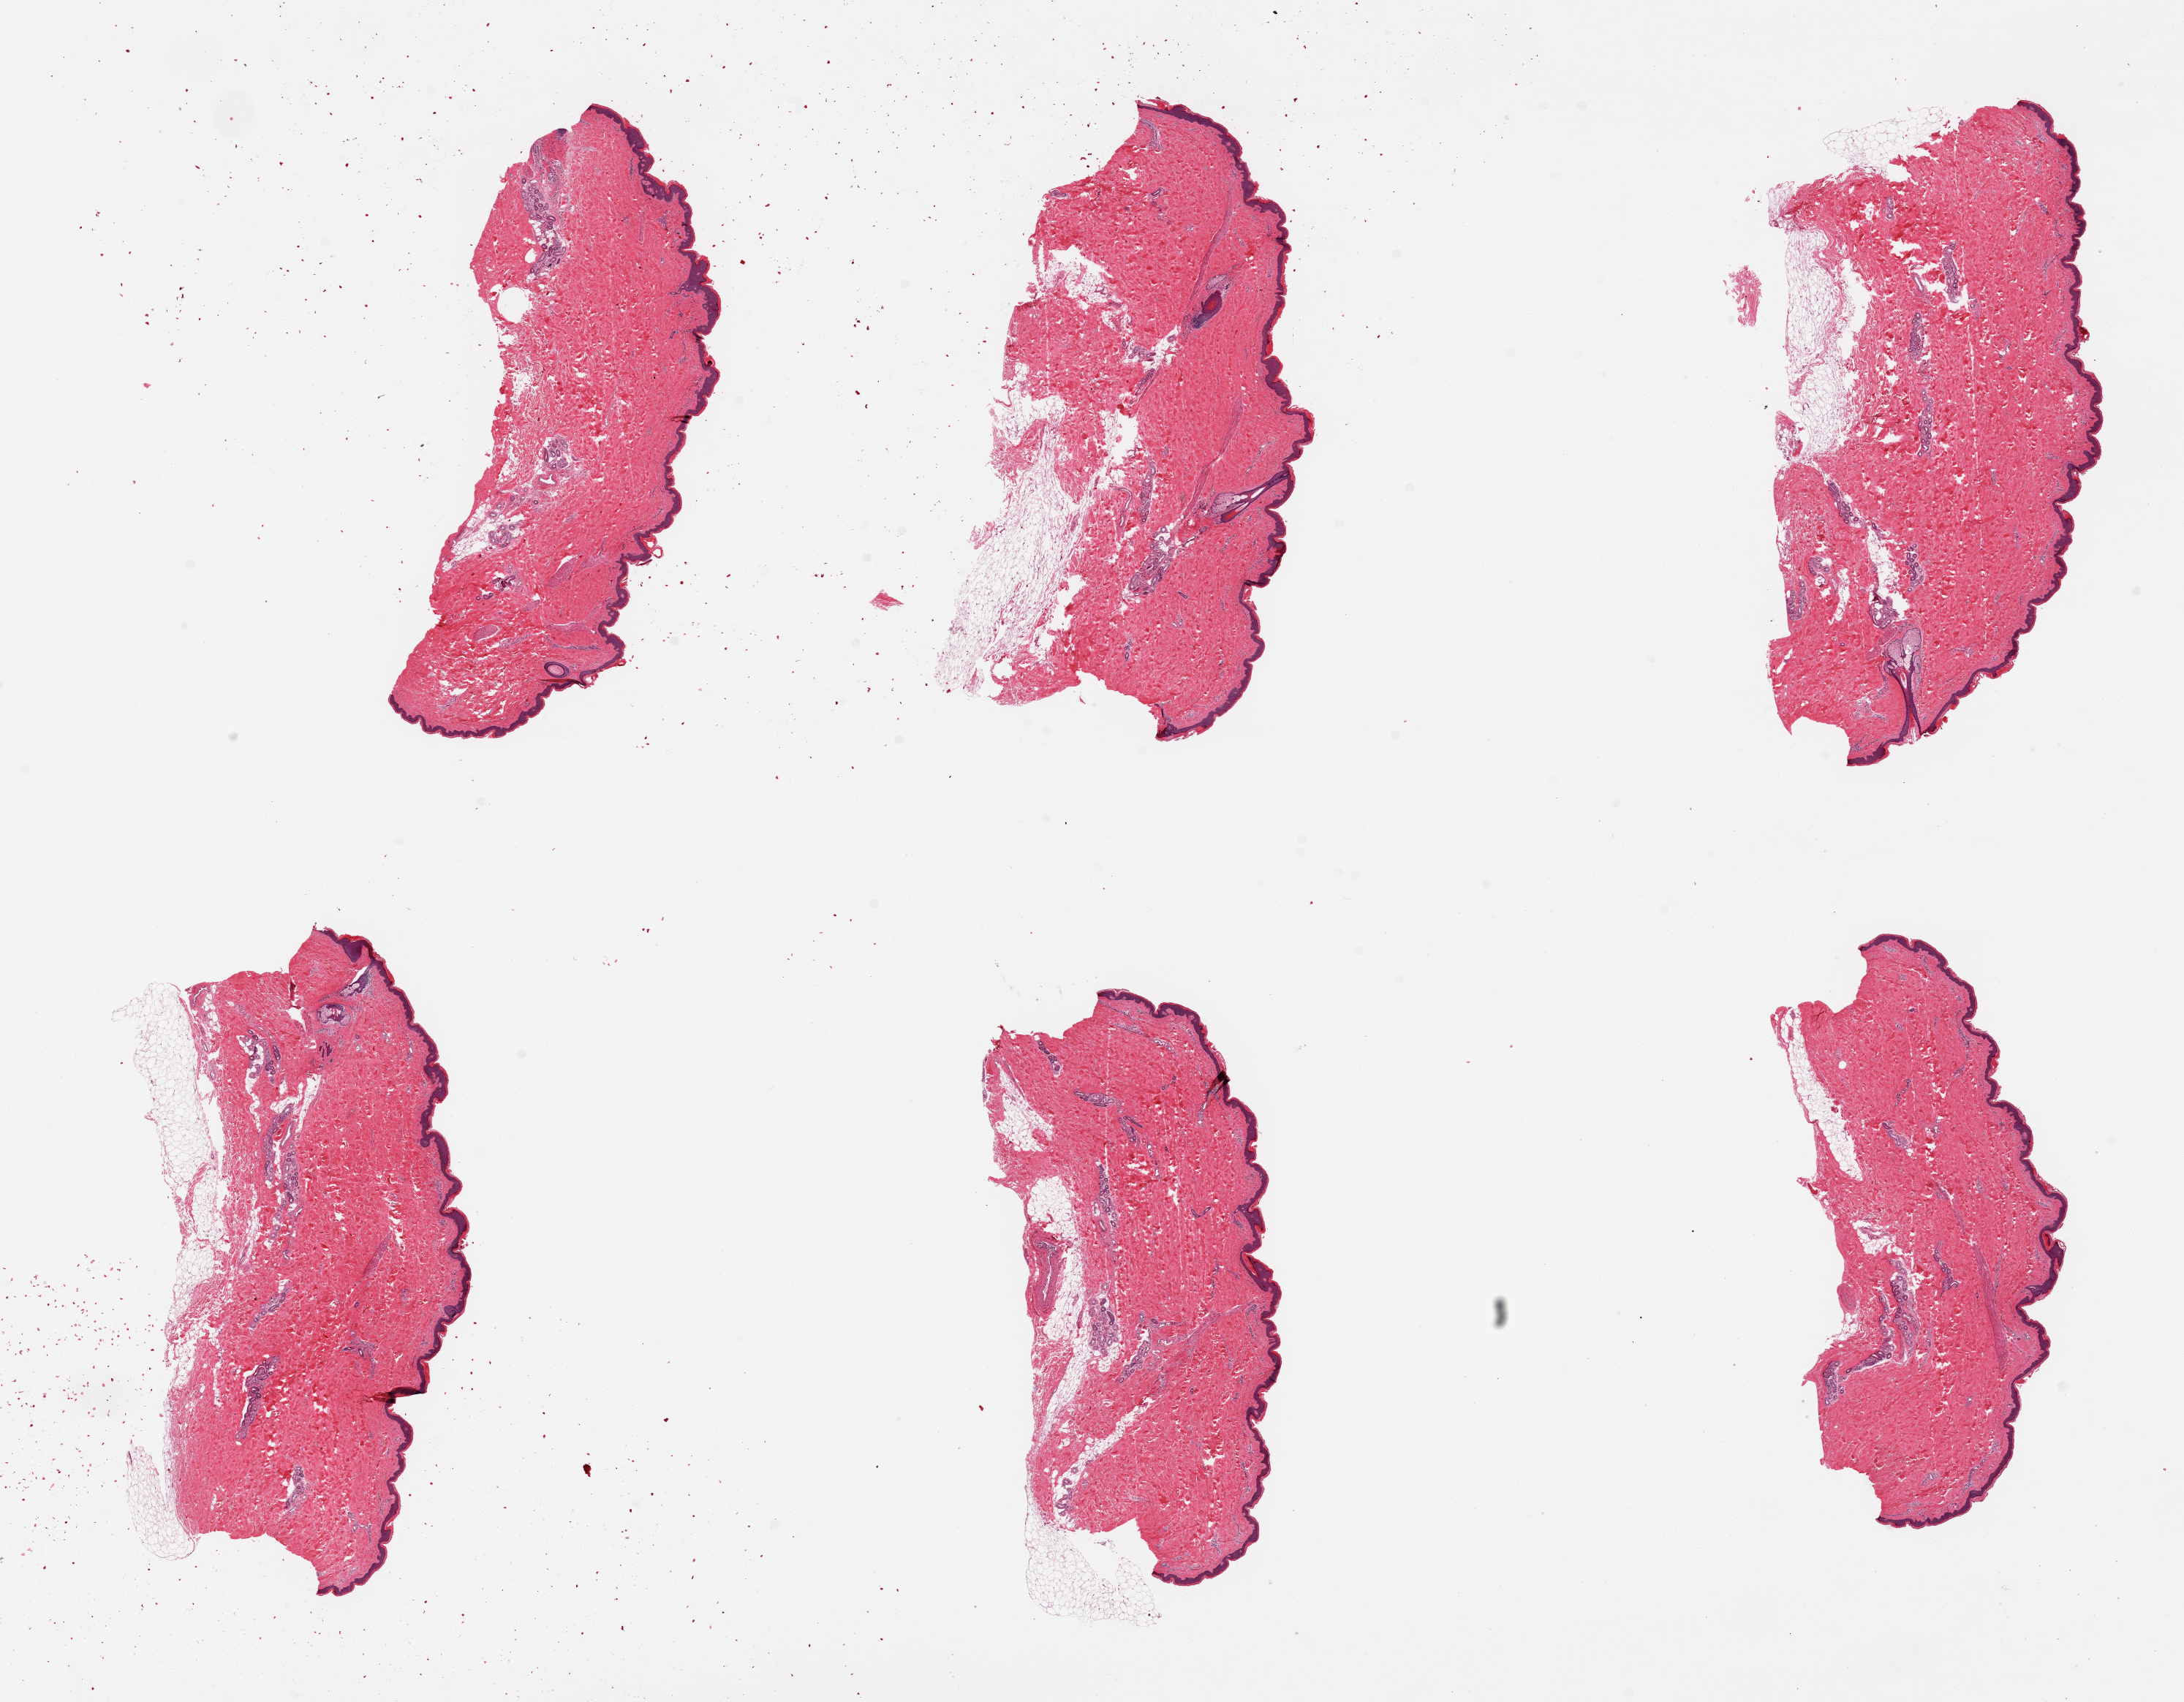
Digitized haematoxylin and eosin-stained section, brightfield, shown as a low-resolution overview of the whole scanned area (about 23.6 x 18.4 mm), PAXgene-fixed, paraffin-embedded tissue, section of skin of lower leg (target tissue), tissue donor sample. Donor: male.
• pathologist's review note for this sample: 6 pieces, up to 7x4mm; squamous epithelium is ~1-2% thickness